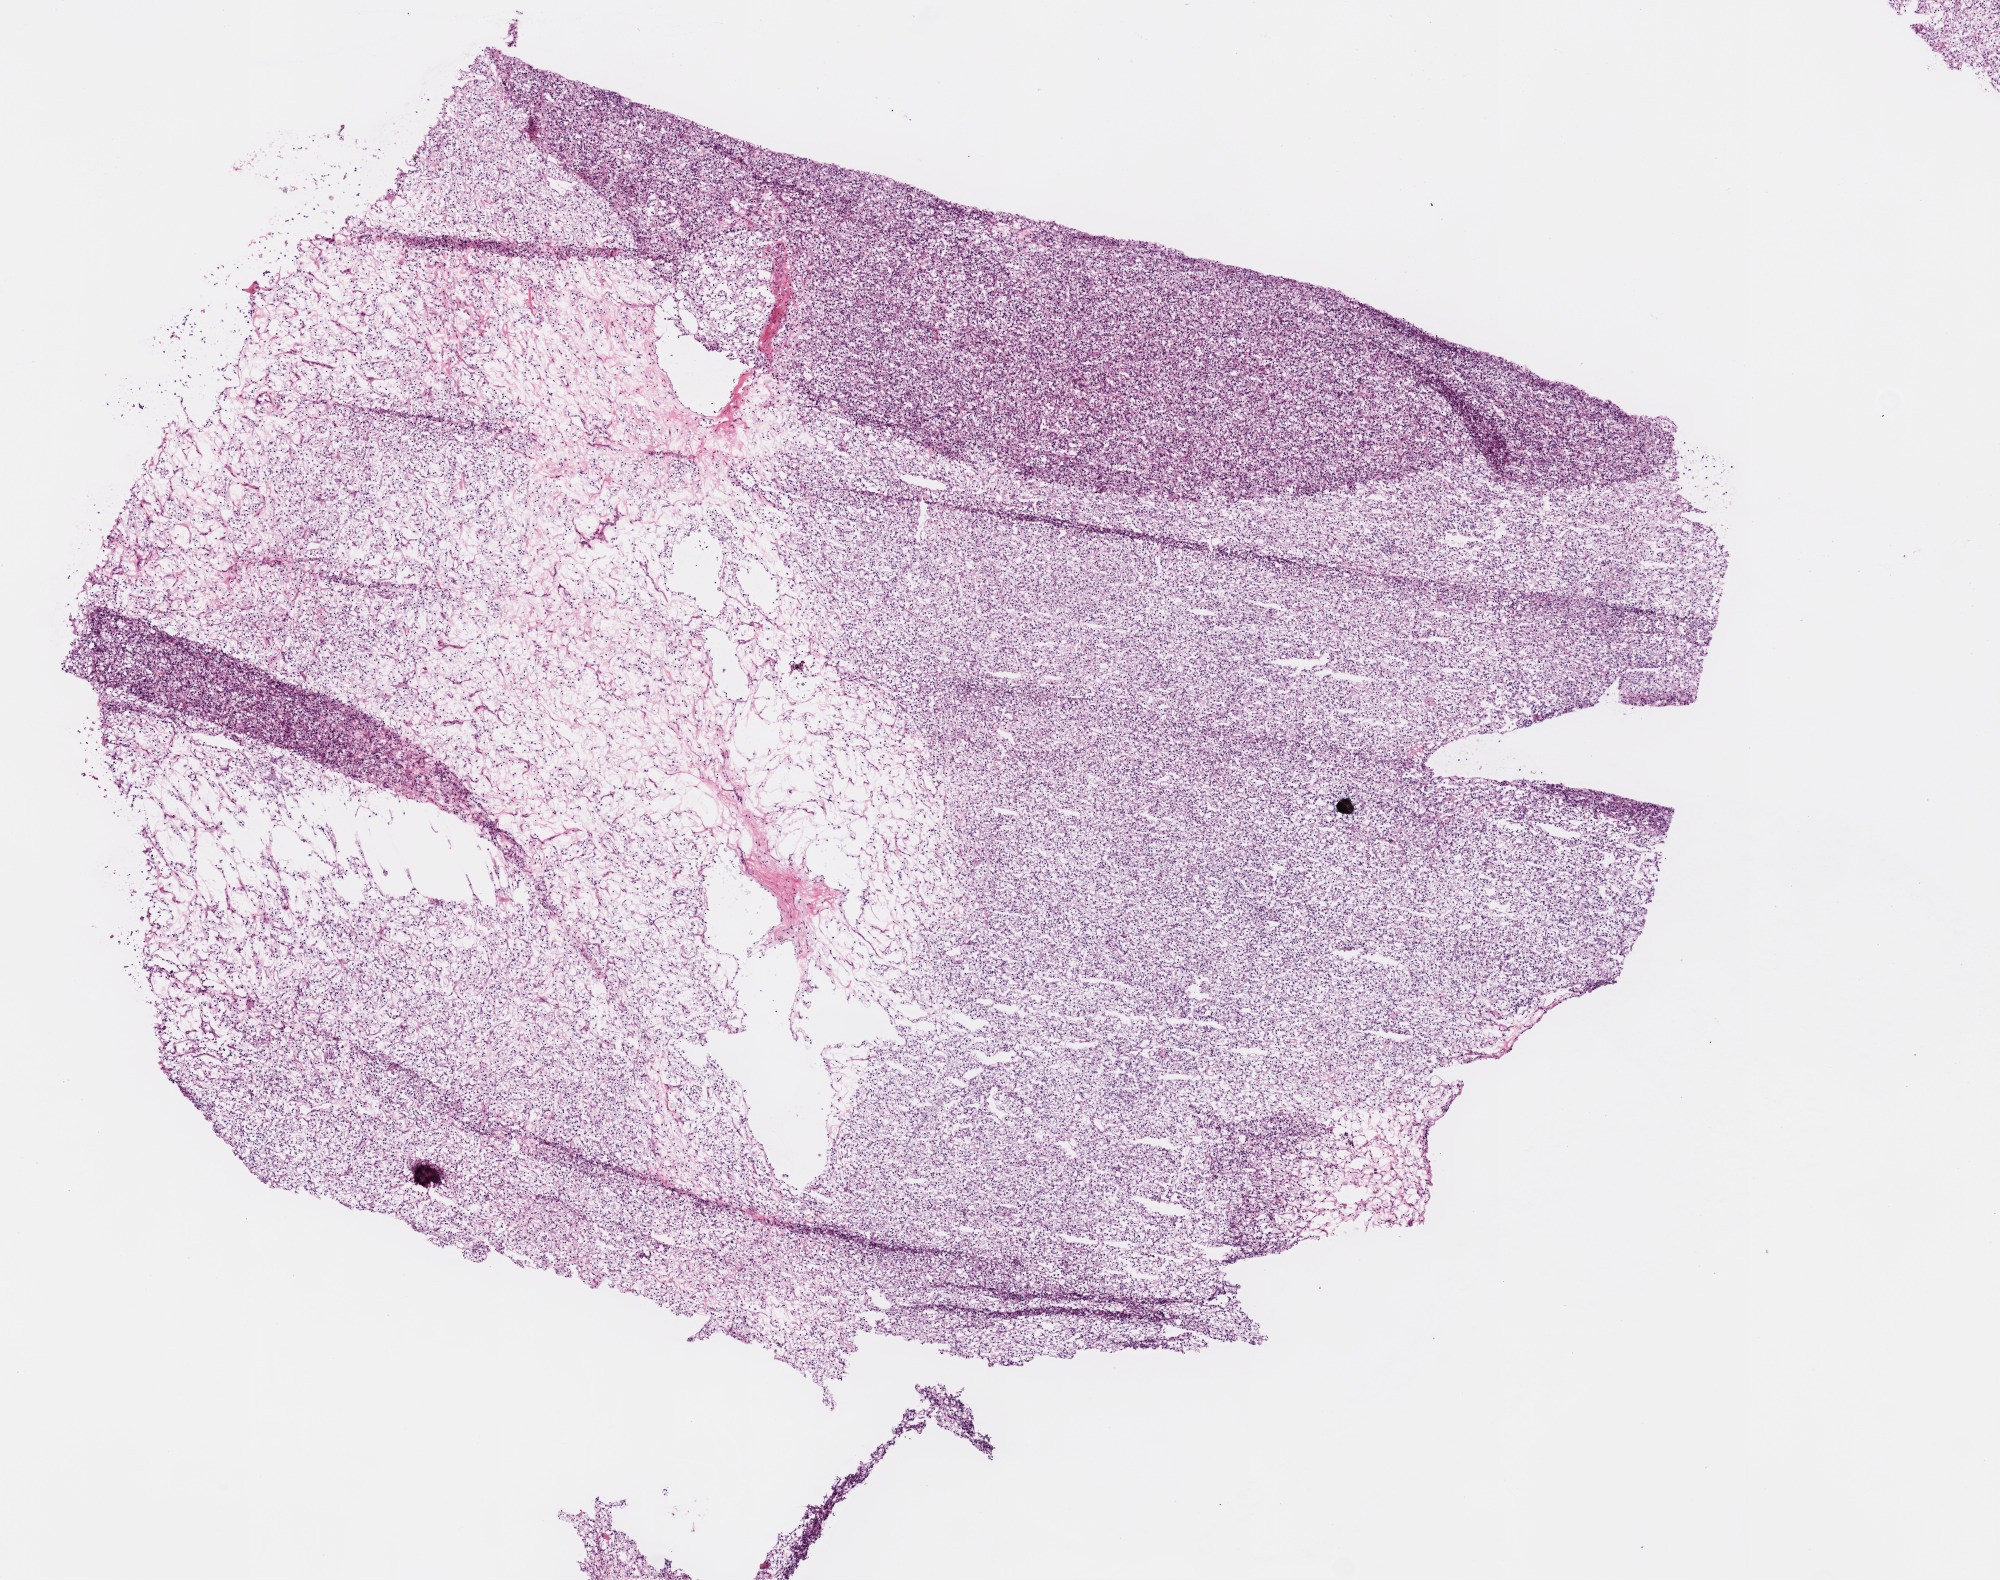
Digitized H&E-stained tissue section (whole slide), a low-resolution overview of the entire scanned area, about 8.0 x 6.3 mm (from a 20x scan); frozen section from the top of the tissue portion; kidney, primary tumour sample. Male, age 52 years at initial diagnosis. Histologic grade: G2 (moderately differentiated). Pathologist review of this section (percent, as recorded): tumour cells 90%, tumour nuclei 85%, normal cells 0%, stromal cells 10%, necrosis 0%.
• TNM: T1 NX M0
• AJCC pathologic stage: I
• diagnosis: Clear cell adenocarcinoma, NOS